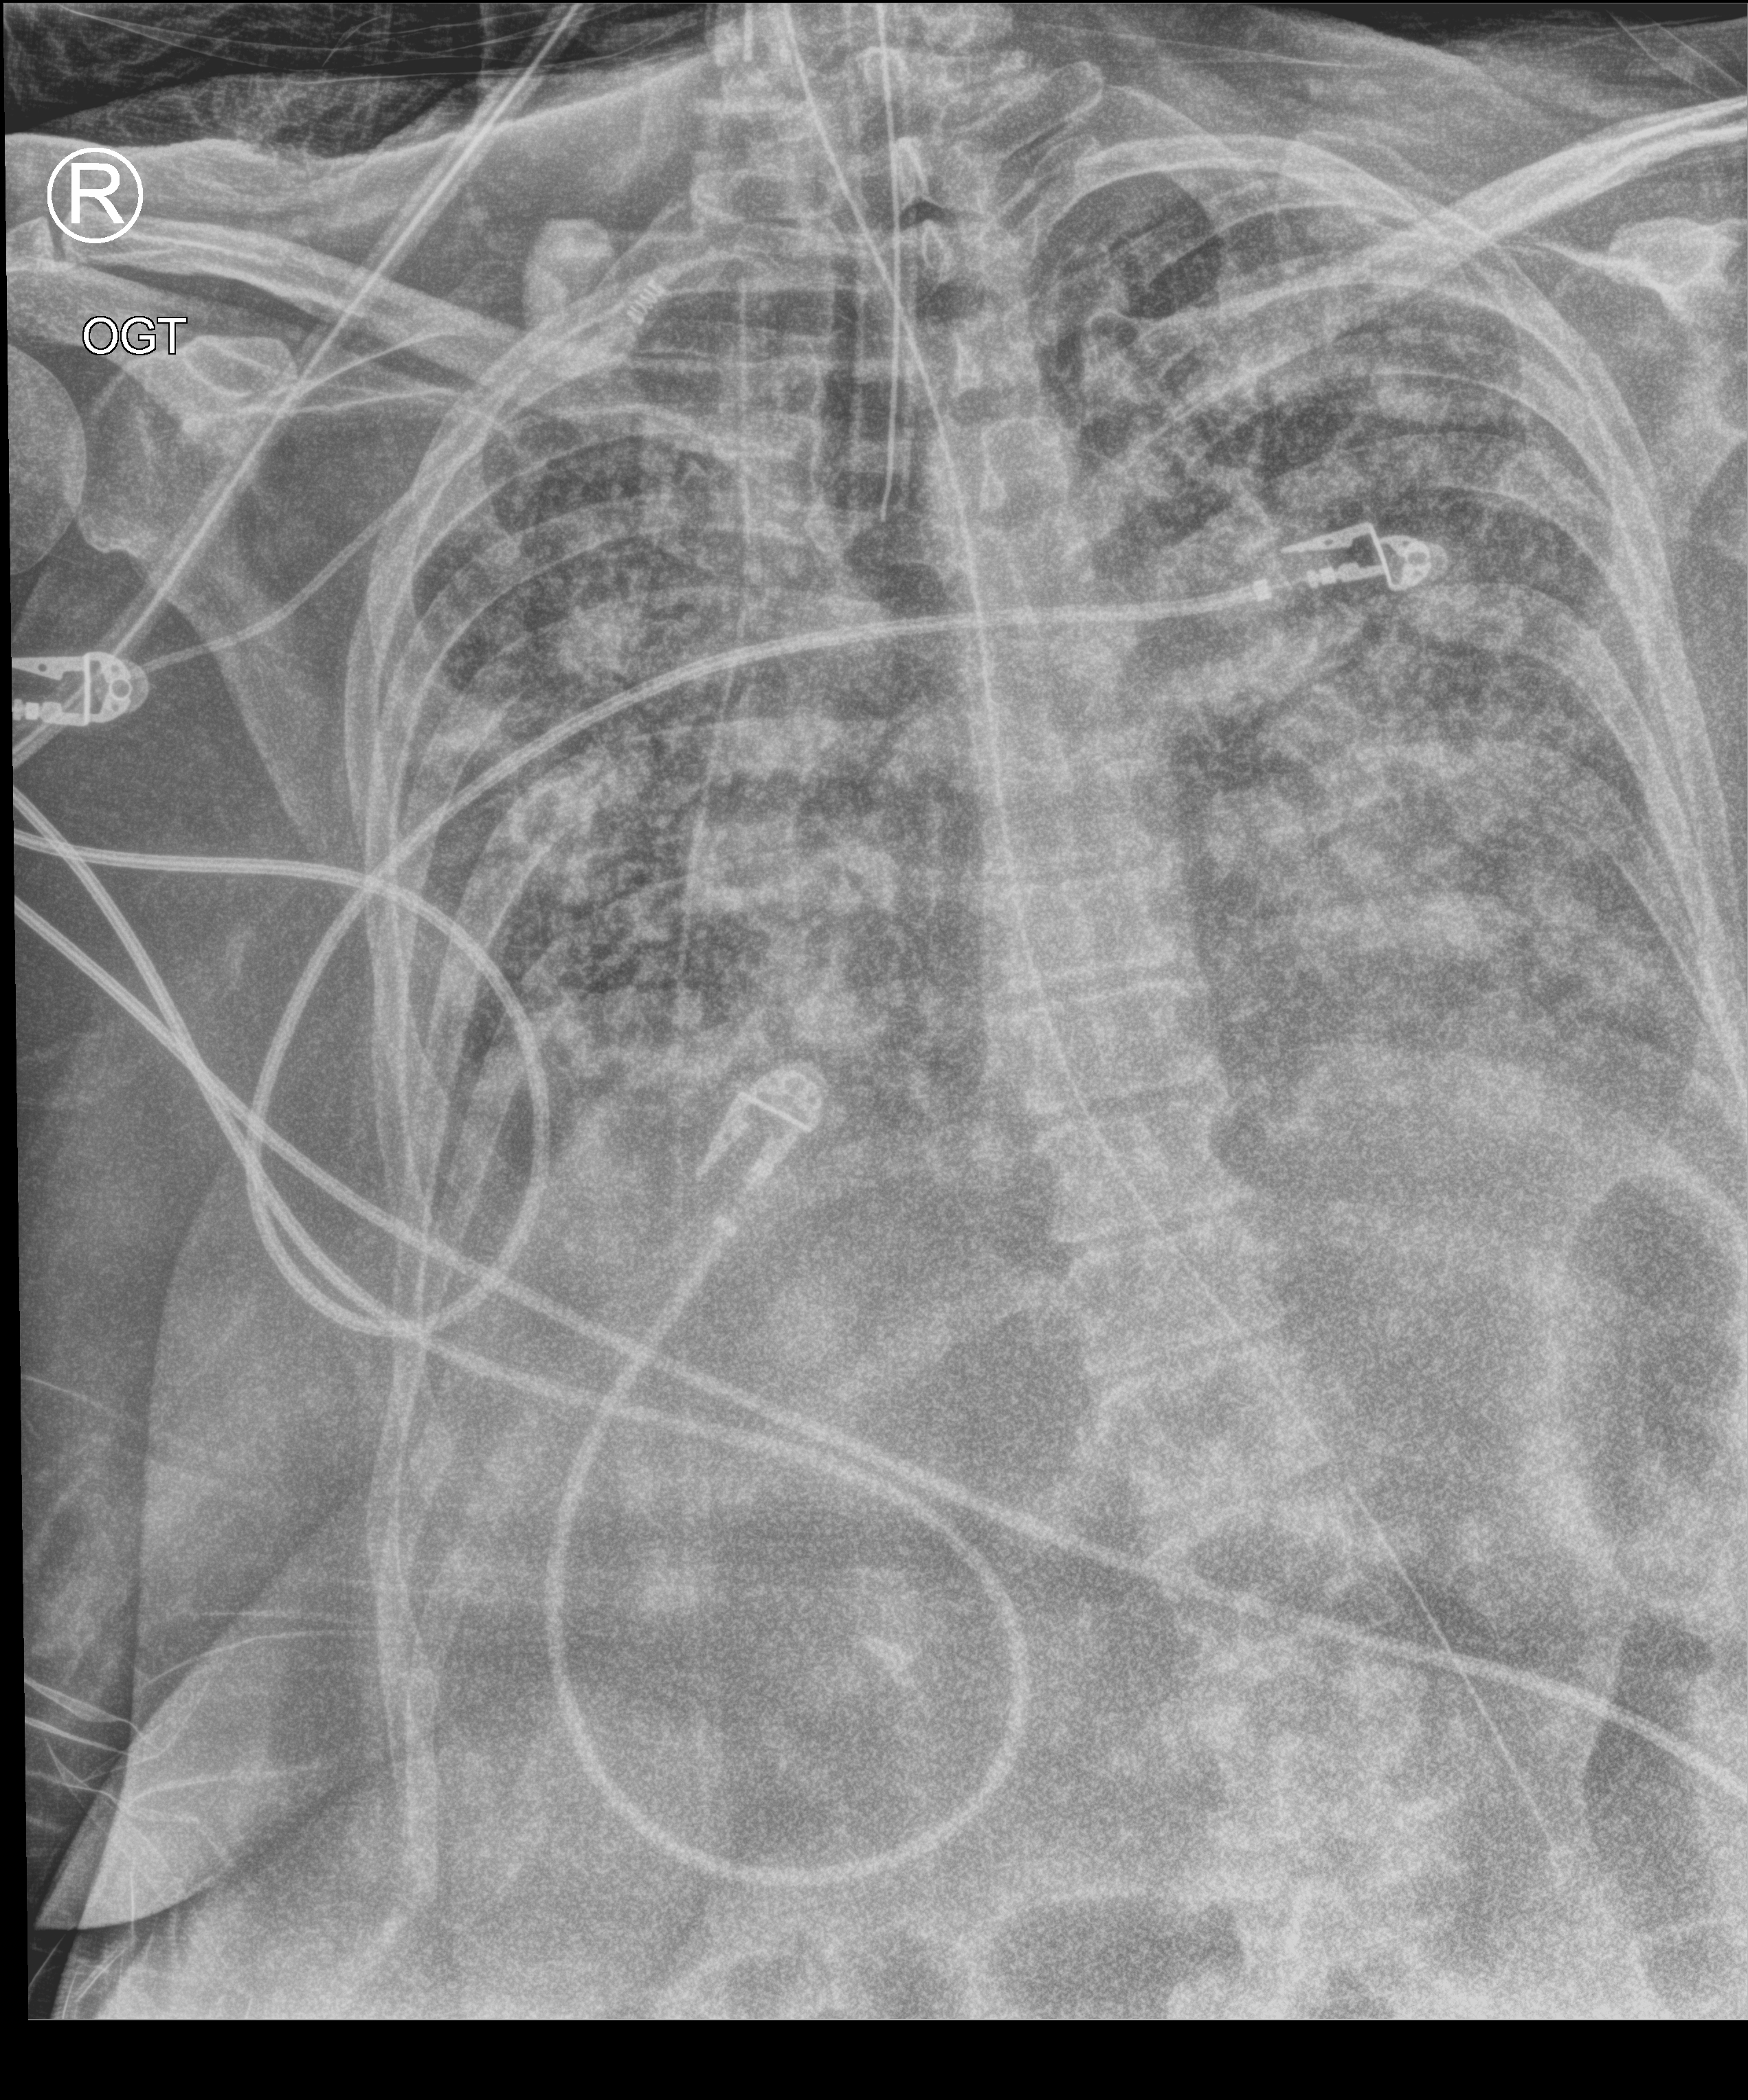
Portable chest radiograph, anteroposterior (AP) projection. Patient hospitalised with COVID-19; female, aged 60–74 years.
Admission-level facts for this patient (not findings on this image; timing relative to this image not recorded):
- mechanically ventilated during this hospital stay: yes